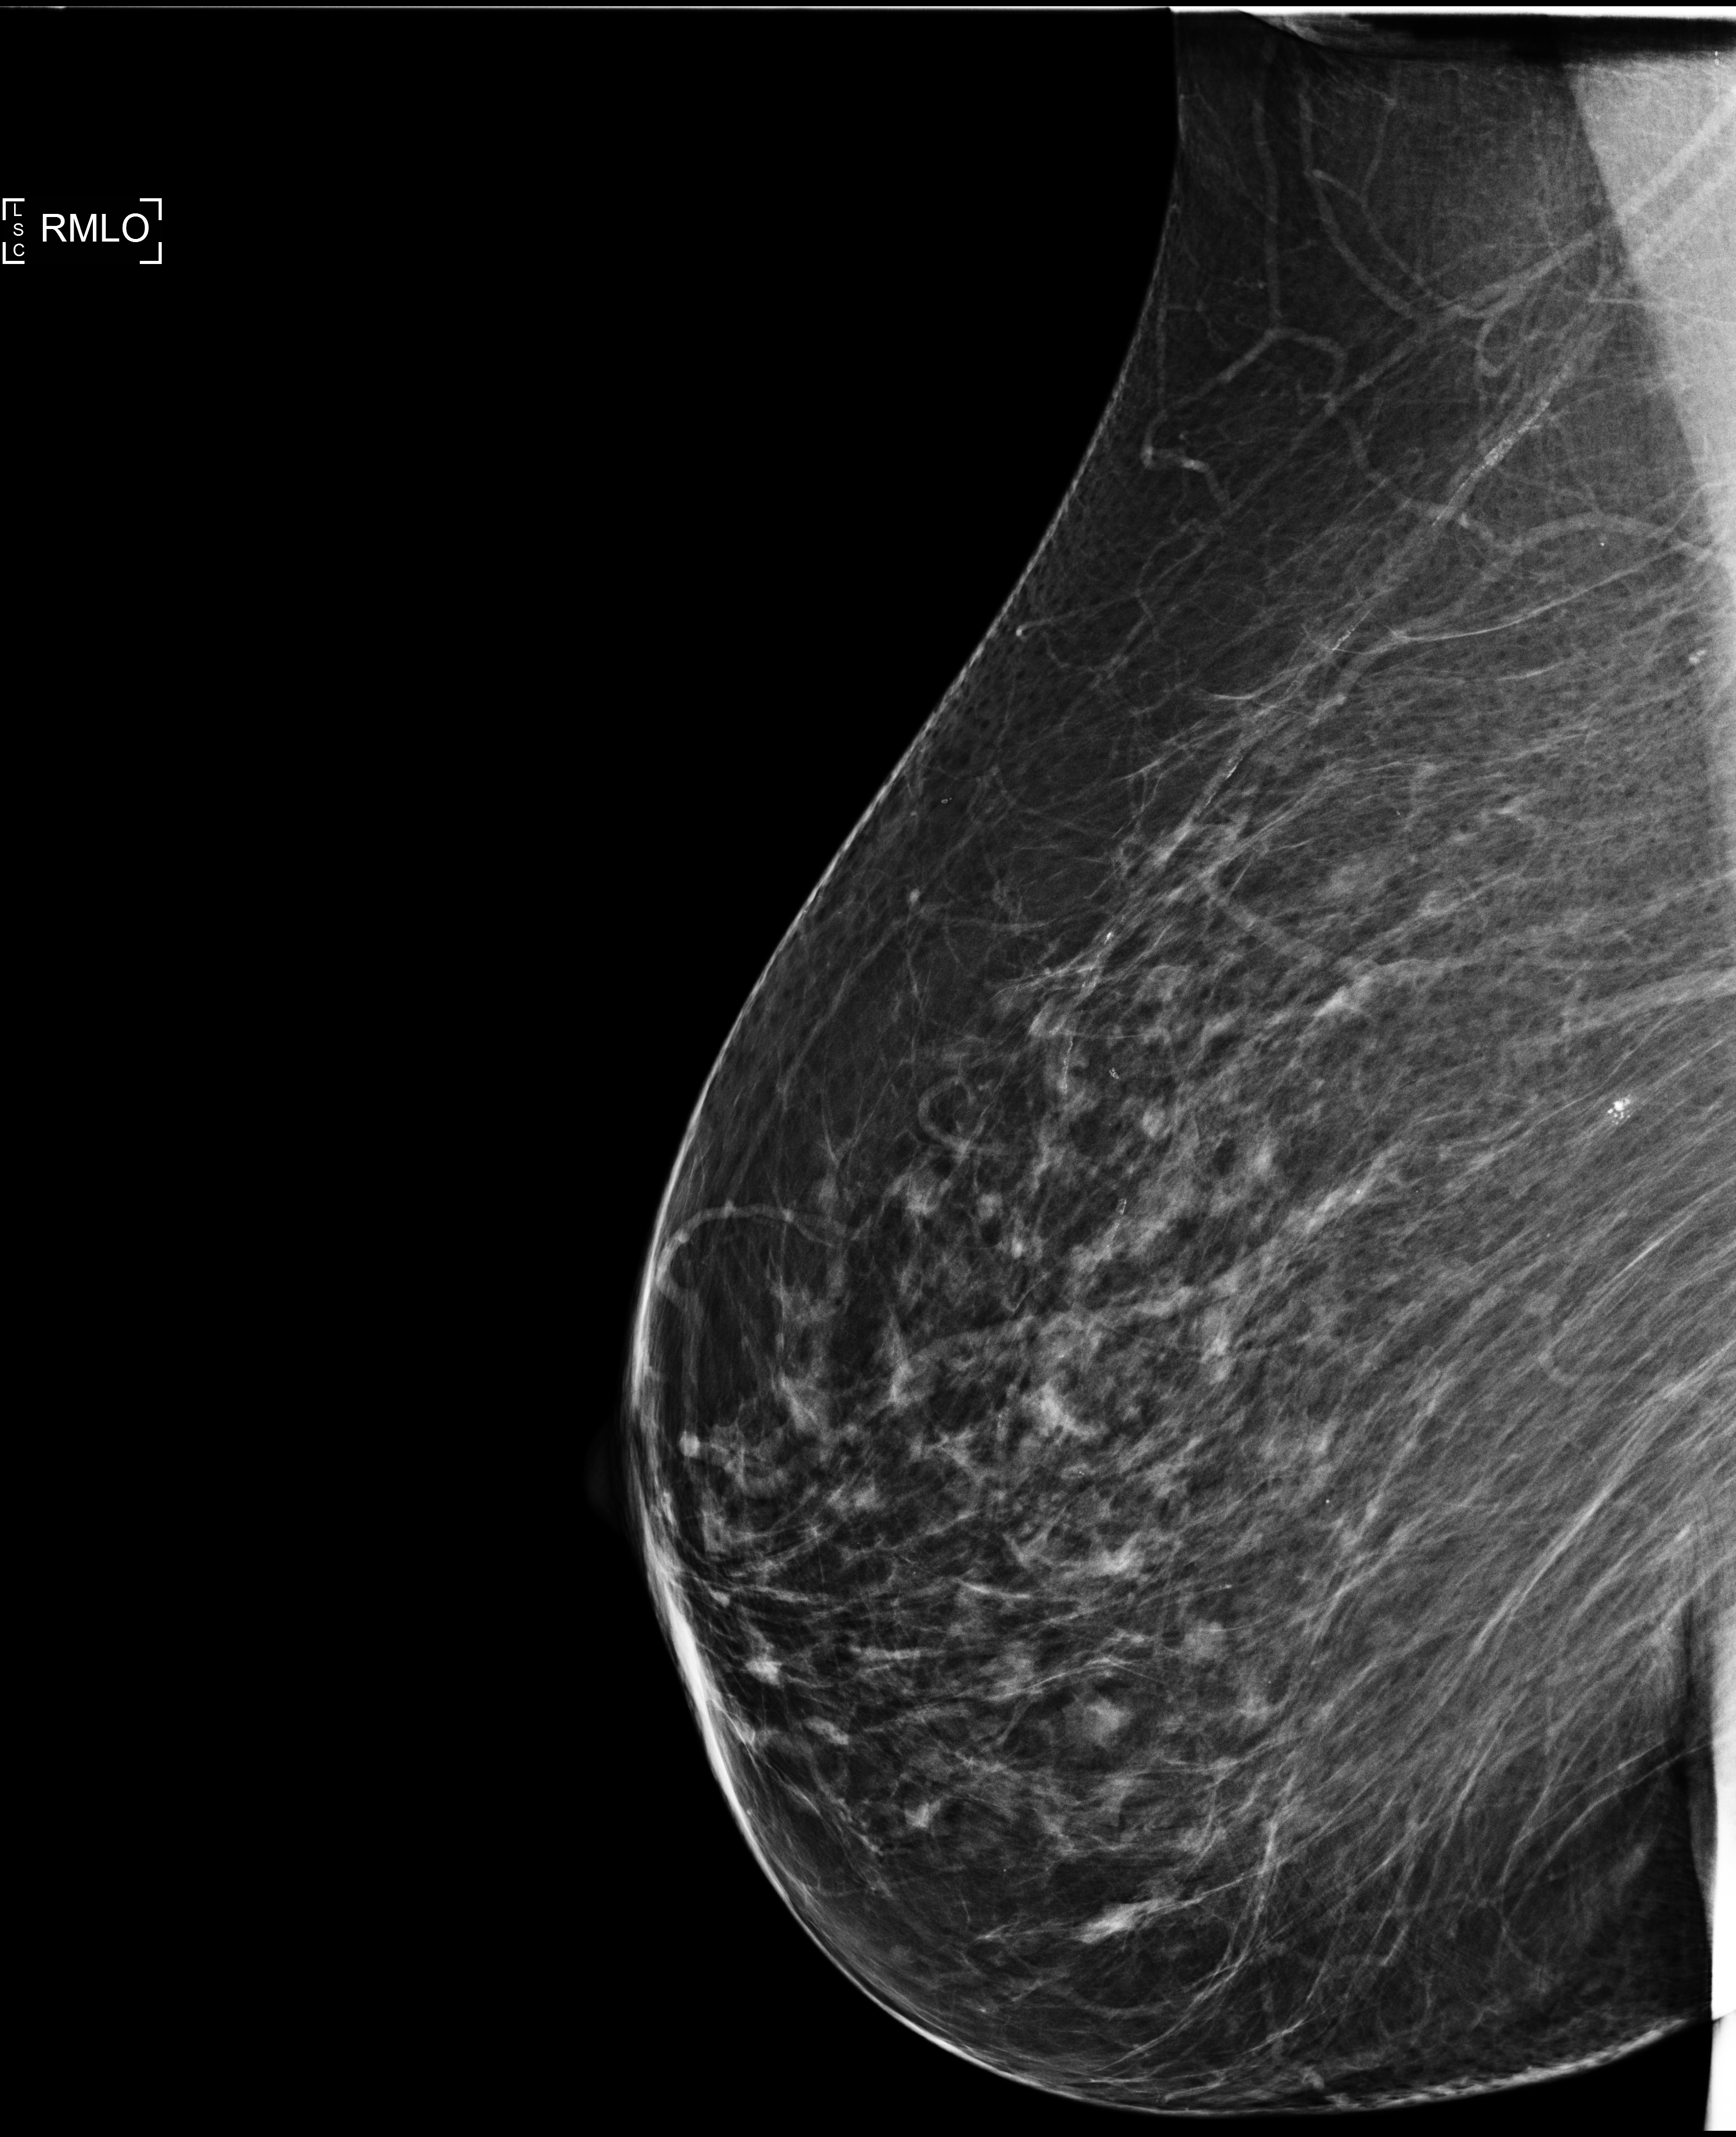
Full-field digital mammogram (FFDM), right breast, mediolateral oblique (MLO) view, screening examination. Female patient, age 73 years.
- BI-RADS breast density category at the screening exam (both breasts, scale 1–4): 3
- final BI-RADS assessment for this screening round (tomosynthesis exam, both breasts): category 1
- recall: no recall after this screen